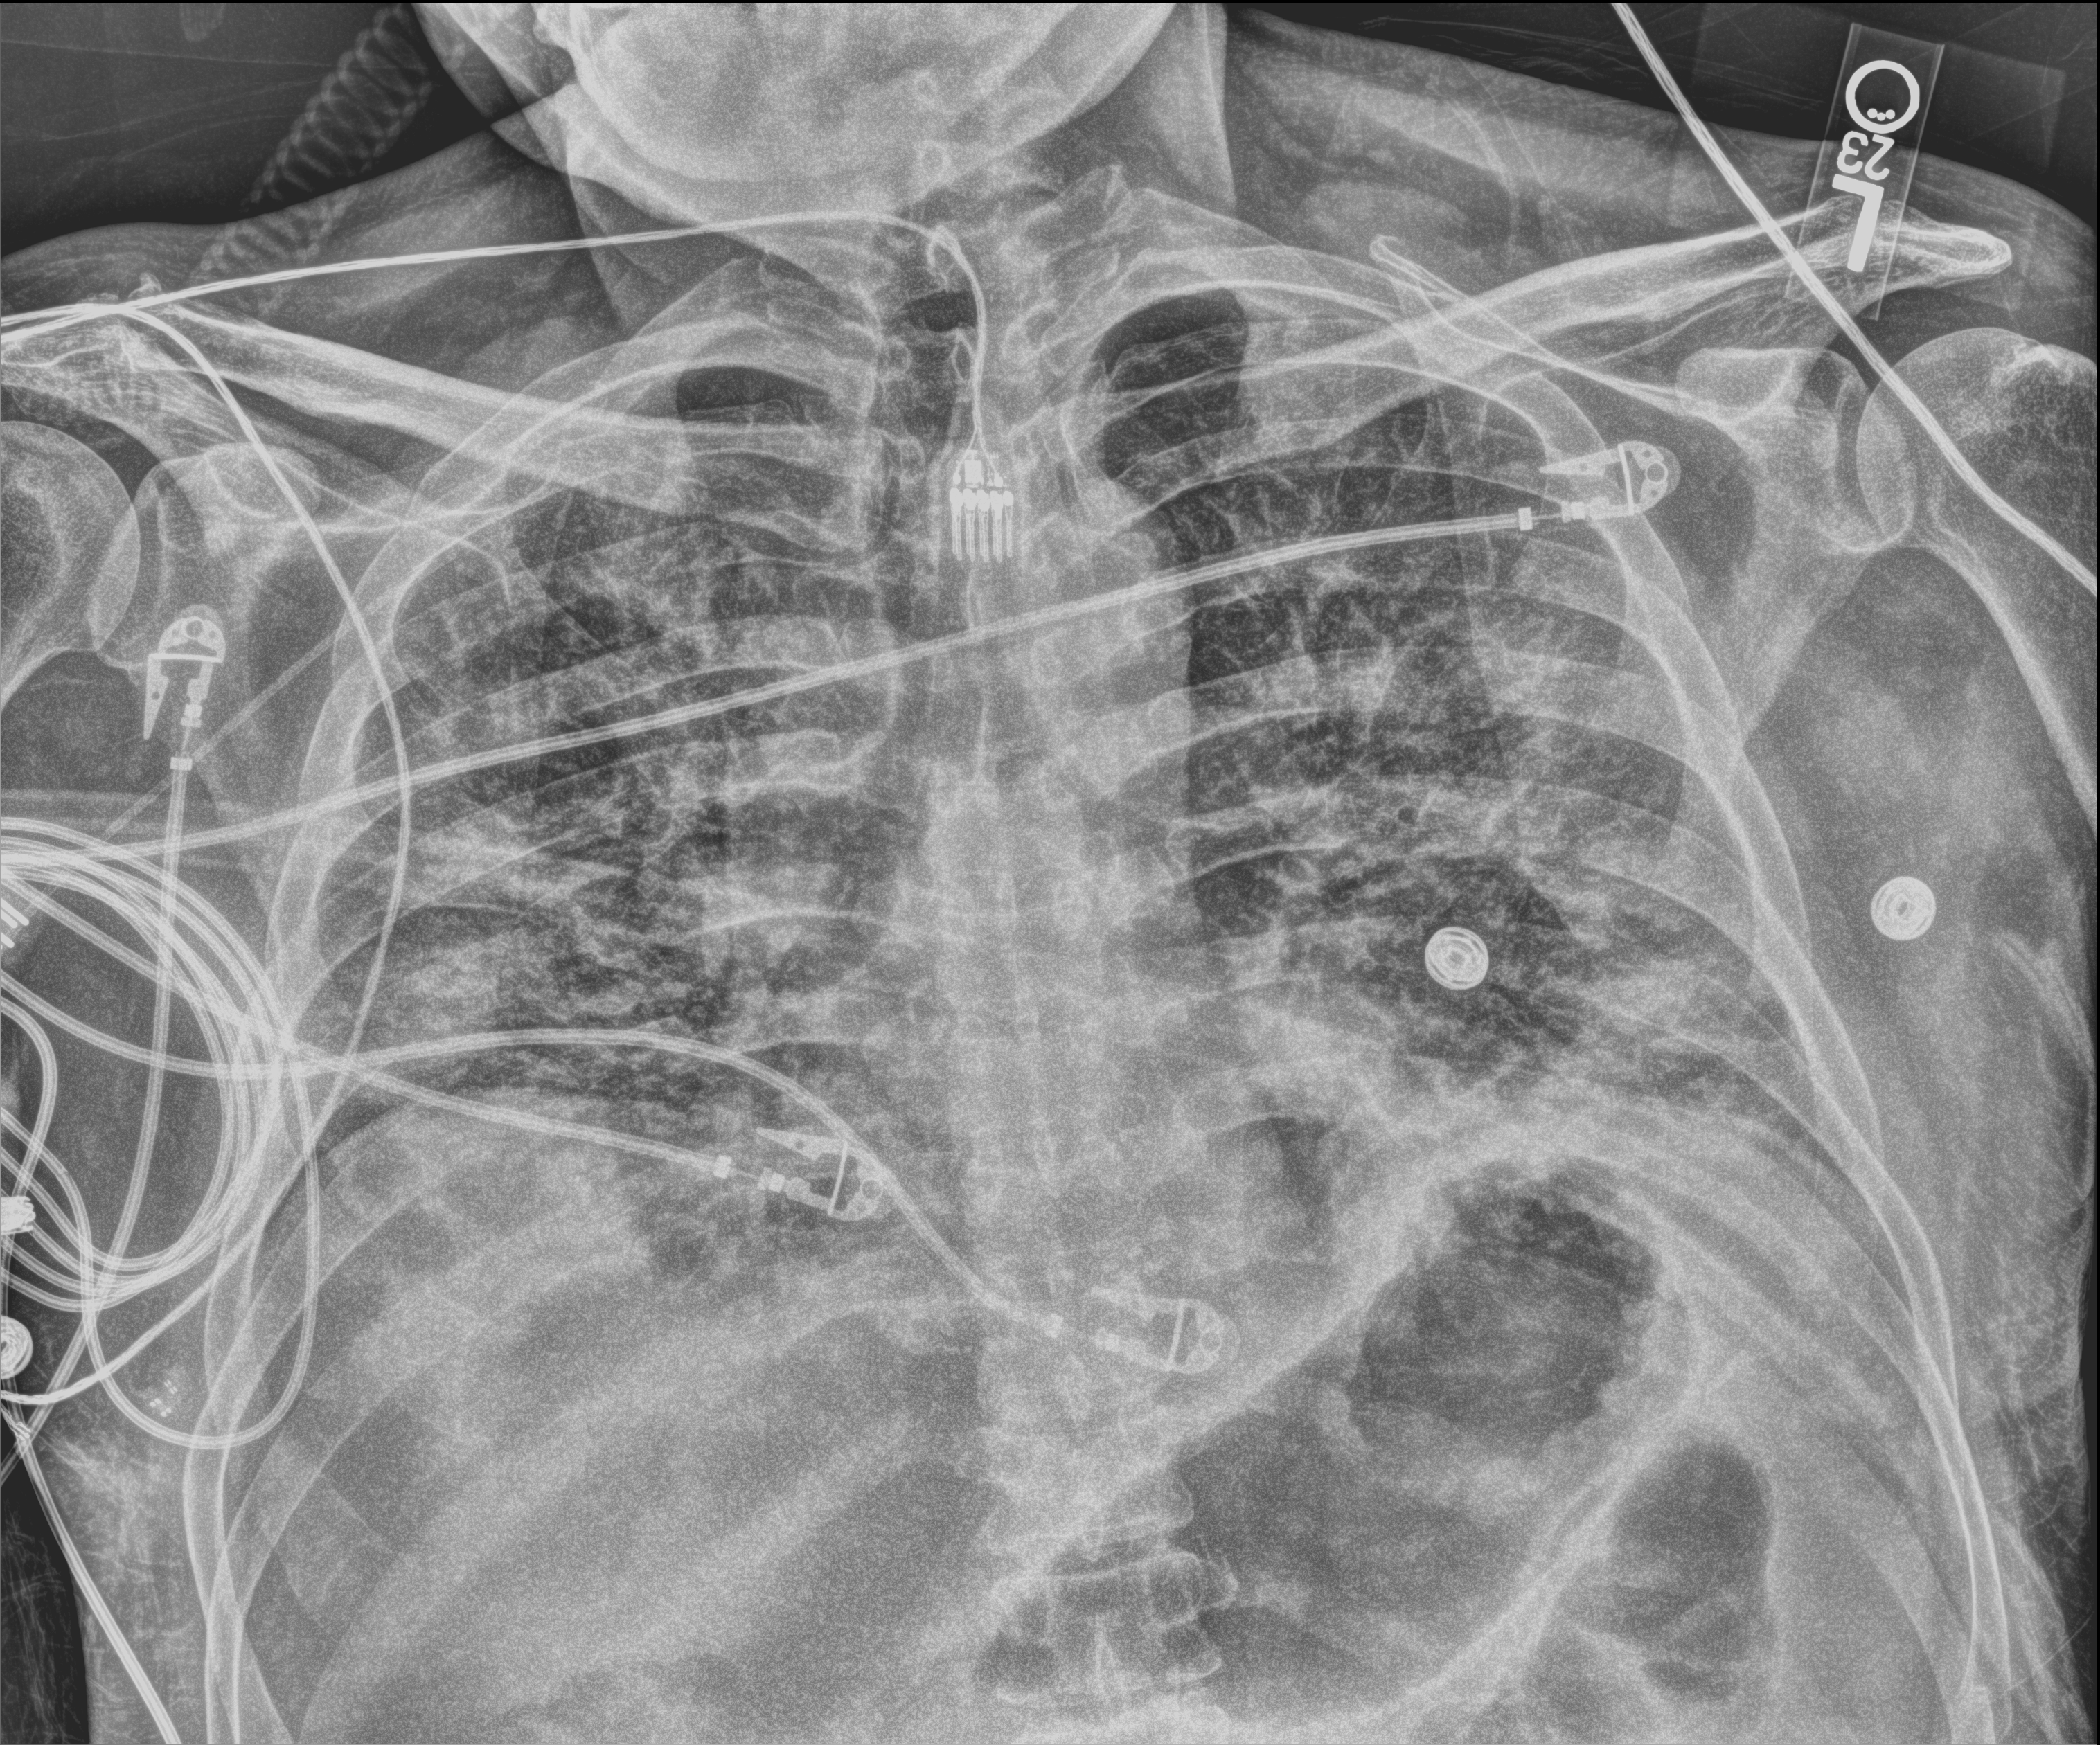
Chest X-ray (portable), anteroposterior (AP) projection. Patient hospitalised with COVID-19; male, aged 18–59 years.
Hospital-stay facts (about this admission, not read from this image; timing relative to this image not recorded): admitted to intensive care during this hospital stay: yes.